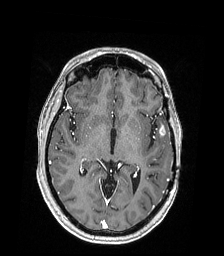
Brain MRI from a brain-tumour surgery series, one axial slice; position 105 of 168 along the scan axis; T1-weighted post-contrast; 224 × 256 image matrix, field of view 224 × 256 mm. Case-level facts recorded for this patient, not image findings: histopathology: Astrocytoma; WHO grade: 4; IDH mutation: yes; tumour location: Left Temporal.
Outlined on this slice (expert manual segmentation):
- tumour: bounding box <152,124,158,136> (left, top, right, bottom; pixels)